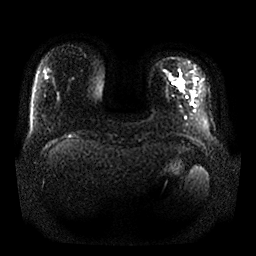
Breast MRI, one axial slice; position 1 of 25 along the scan axis; diffusion-weighted series; image 2 of 4 stored at this slice position (different b-values; order by instance number); 1.5 T; 4 mm slice thickness; 256 × 256 image matrix, field of view 380 × 380 mm. Female patient.
Annotated regions visible in this slice (expert manual segmentation):
- tumour on diffusion-weighted imaging: bounding box <179,79,184,92> (left, top, right, bottom; pixels)